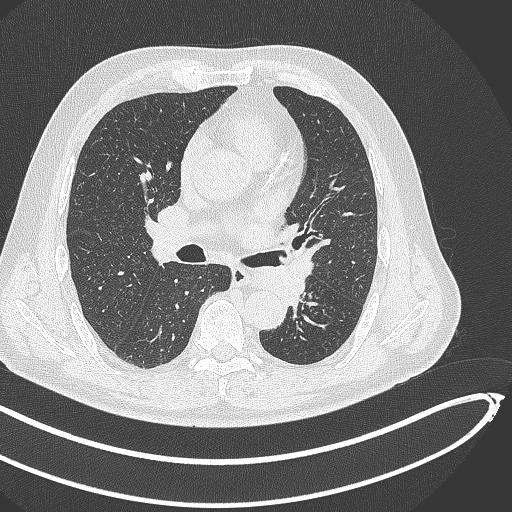
Chest CT, one axial slice. Slice 261 of 468 in the series (ordered by position). Lung window (W 1500 / L -600 HU). 512 × 512 image matrix, field of view 400 × 400 mm. Patient: male, 64 years. From the clinical record (not read from this slice): clinical TNM (as recorded): T1c N0 M0.
Annotated regions visible in this slice (rectangle marked by the reading radiologist):
- lung tumour (recorded histology: squamous cell carcinoma): box from (x=247, y=250) to (x=320, y=306) px